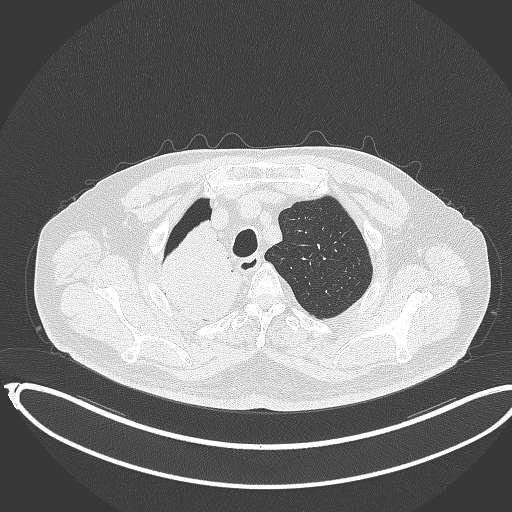
Chest CT, one axial slice; position 310 of 403 along the scan axis; reconstruction kernel B70f; lung window (W 1500 / L -600 HU); 1 mm slice thickness; 512 × 512 image matrix, field of view 436 × 436 mm. Patient: male, 68 years. From the clinical record (not read from this slice): clinical TNM (as recorded): T2a N0 M0.
Annotated regions visible in this slice (rectangle marked by the reading radiologist):
- lung tumour (recorded histology: adenocarcinoma): bounding box <150,216,245,324> (left, top, right, bottom; pixels)